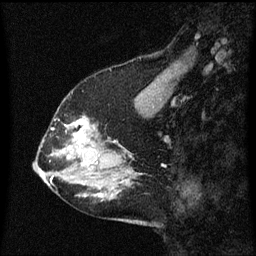
Breast MRI (dynamic contrast-enhanced), one sagittal slice; dynamic contrast-enhanced series, image 2 of 3 at this slice position (ordered by acquisition); 1.5 T; TE 4.2 ms, TR 8.4 ms; 2 mm slice thickness; 256 × 256 image matrix. Female patient, age 58 years.
Annotated regions visible in this slice (semi-automatic segmentation, software-assisted and operator-edited):
- analysis volume of interest (the breast-tissue region the enhancement analysis was run in; not a lesion): bounding box <58,118,99,151> (left, top, right, bottom; pixels)
- tumour enhancement mask (voxels above the 70 % enhancement threshold inside the analysis volume of interest): <68,120,91,151>